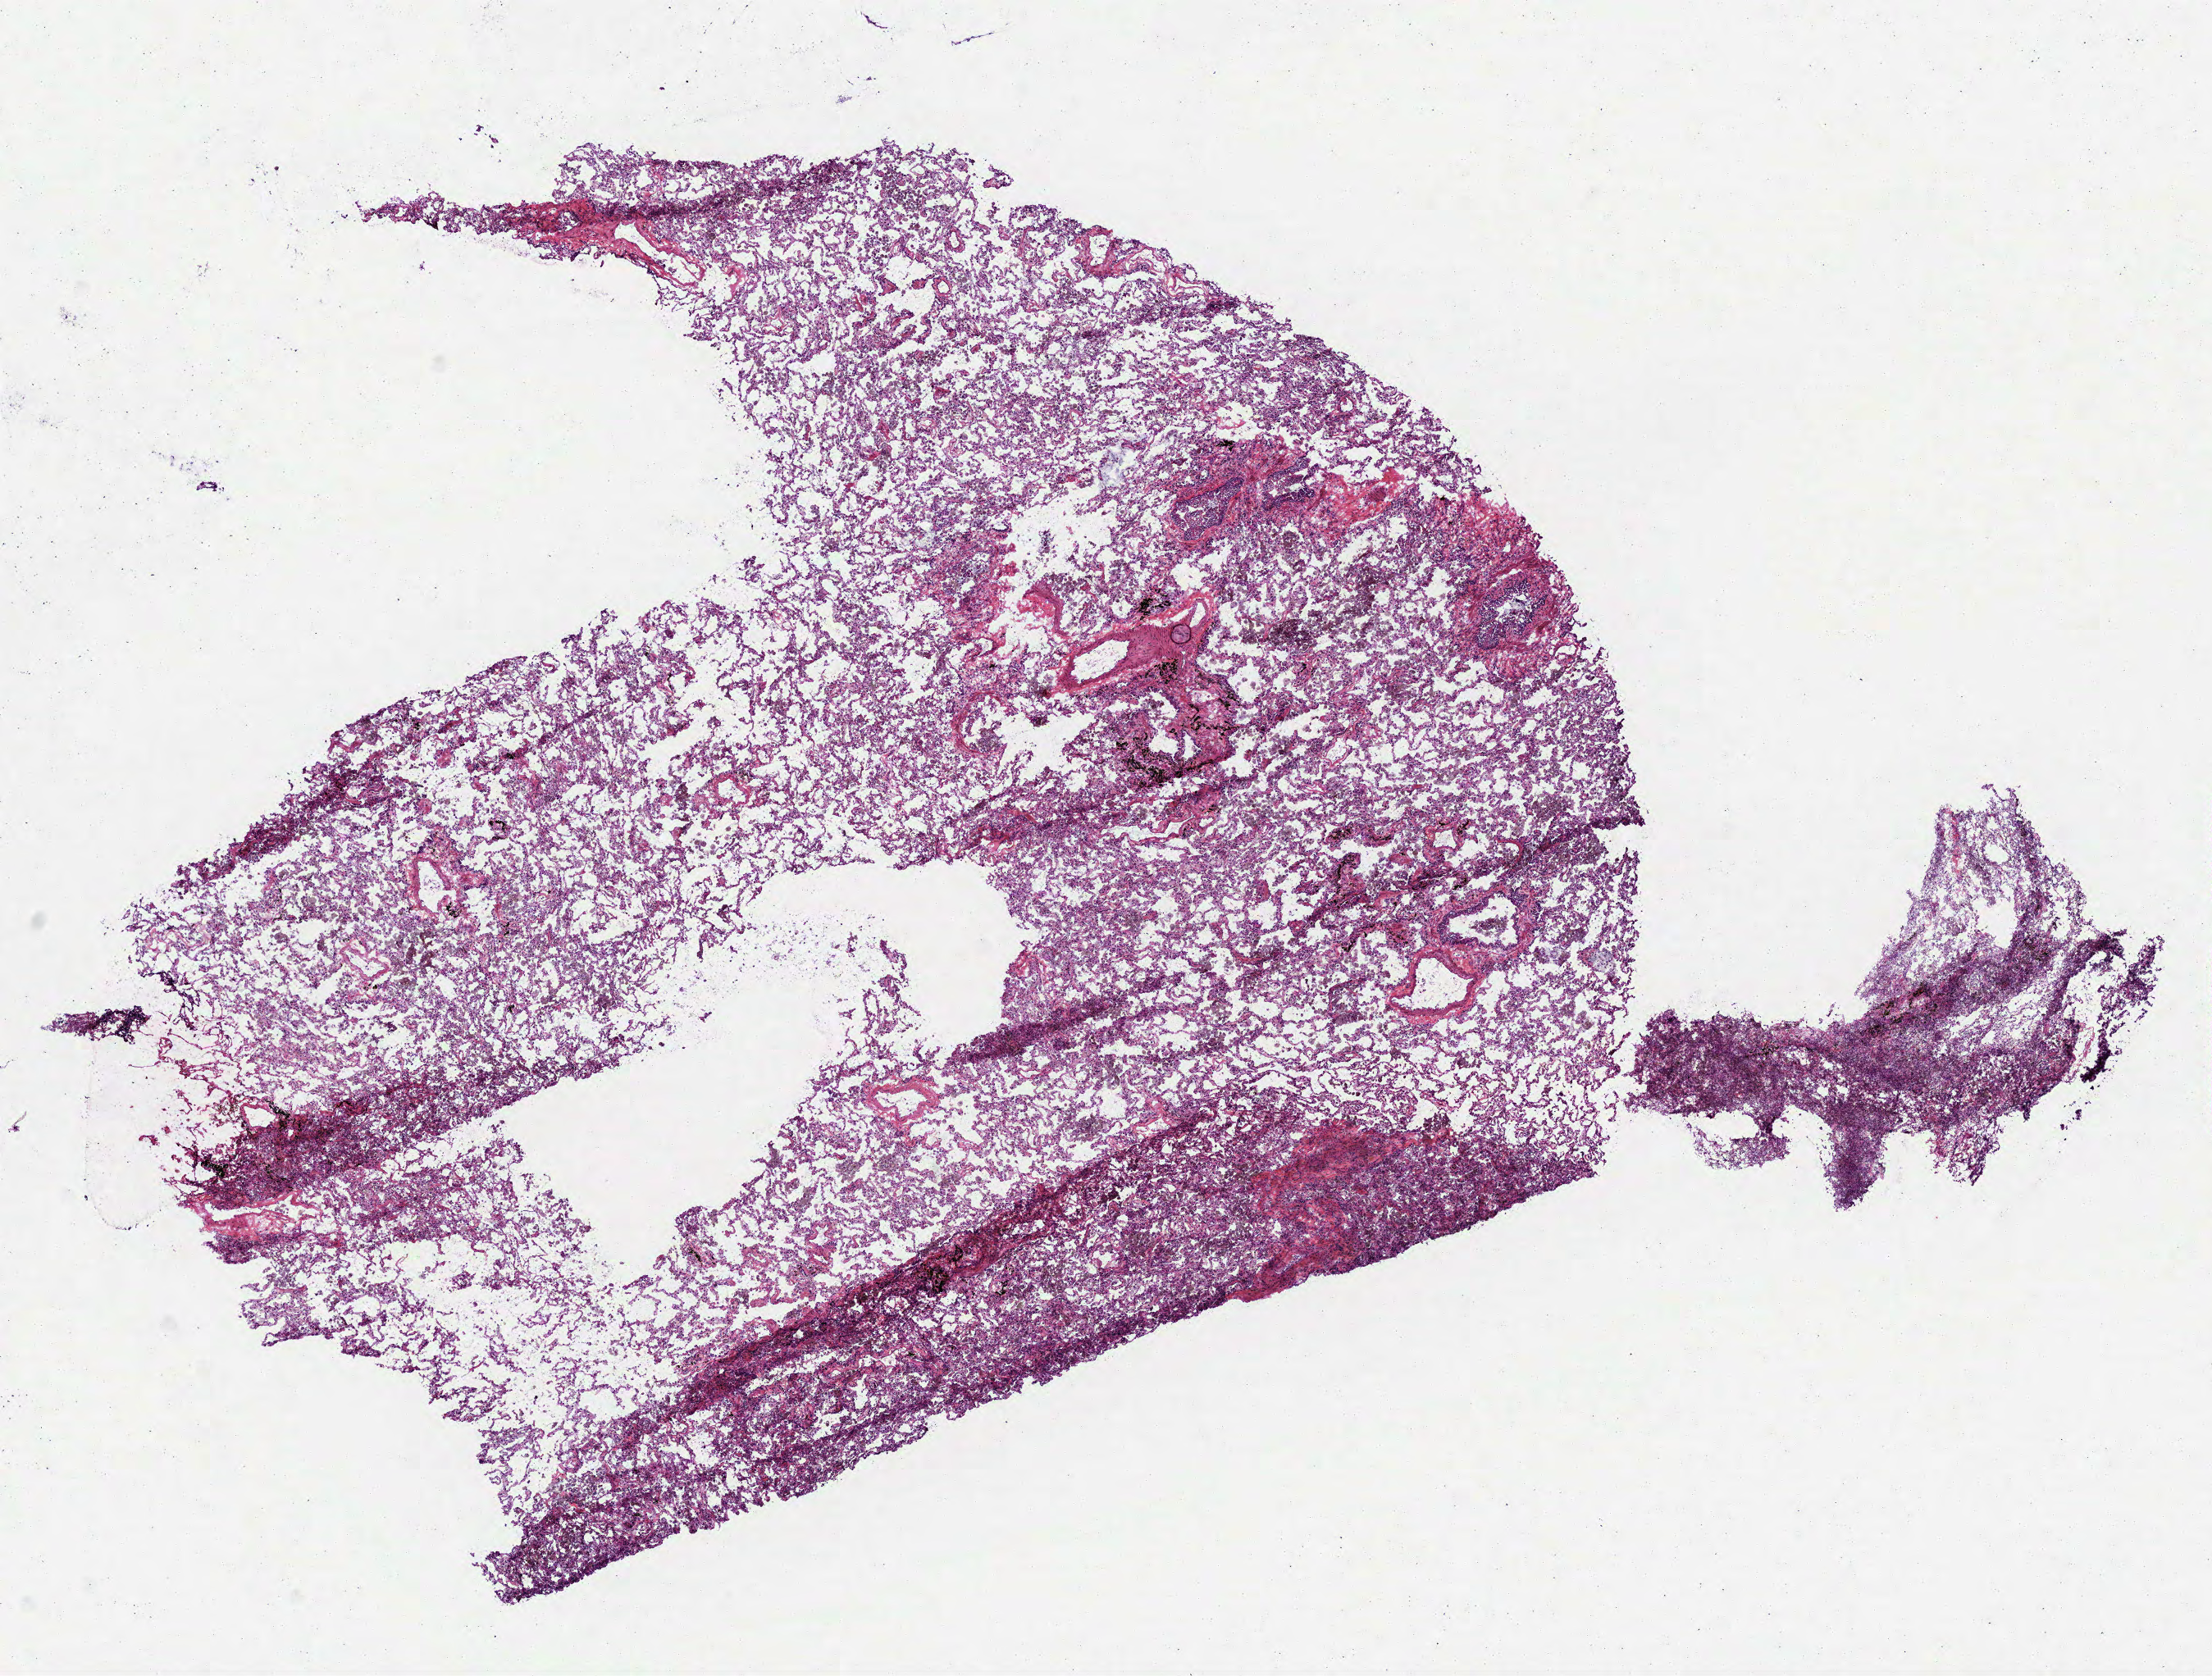
Hematoxylin and eosin (H&E) stained whole-slide image — a low-resolution overview of the entire scanned area, about 10.9 x 8.2 mm (slide scanned at 40x); frozen section; solid tissue normal (non-tumour tissue) sample from the lung. Male, age 41 years at initial diagnosis.
This section: solid tissue normal (non-tumour) sample from the same patient. Patient diagnosis: Bronchiolo-alveolar carcinoma, non-mucinous.